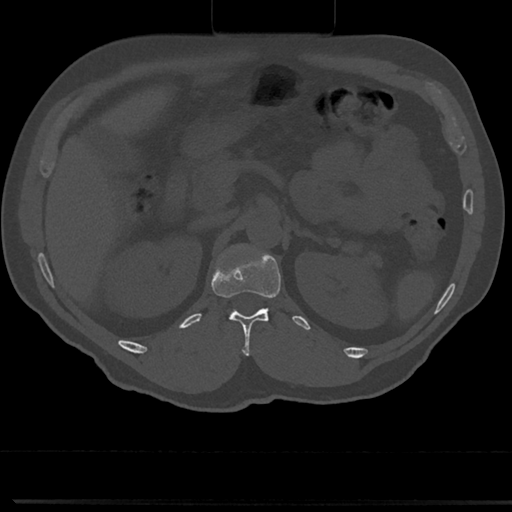
CT including the spine, one axial slice; slice 131 of 817 in the series (ordered by position); reconstruction kernel Br40s/3; 120 kVp; bone window (W 1800 / L 400 HU); 0.5 mm slice thickness; 512 × 512 image matrix, field of view 355 × 355 mm. Patient: male, 61 years. Case-level facts recorded for this patient, not image findings: primary cancer: prostate.
Outlined on this slice (semi-automatically segmented with operator editing):
- T12 vertebra: box from (x=221, y=266) to (x=282, y=357) px